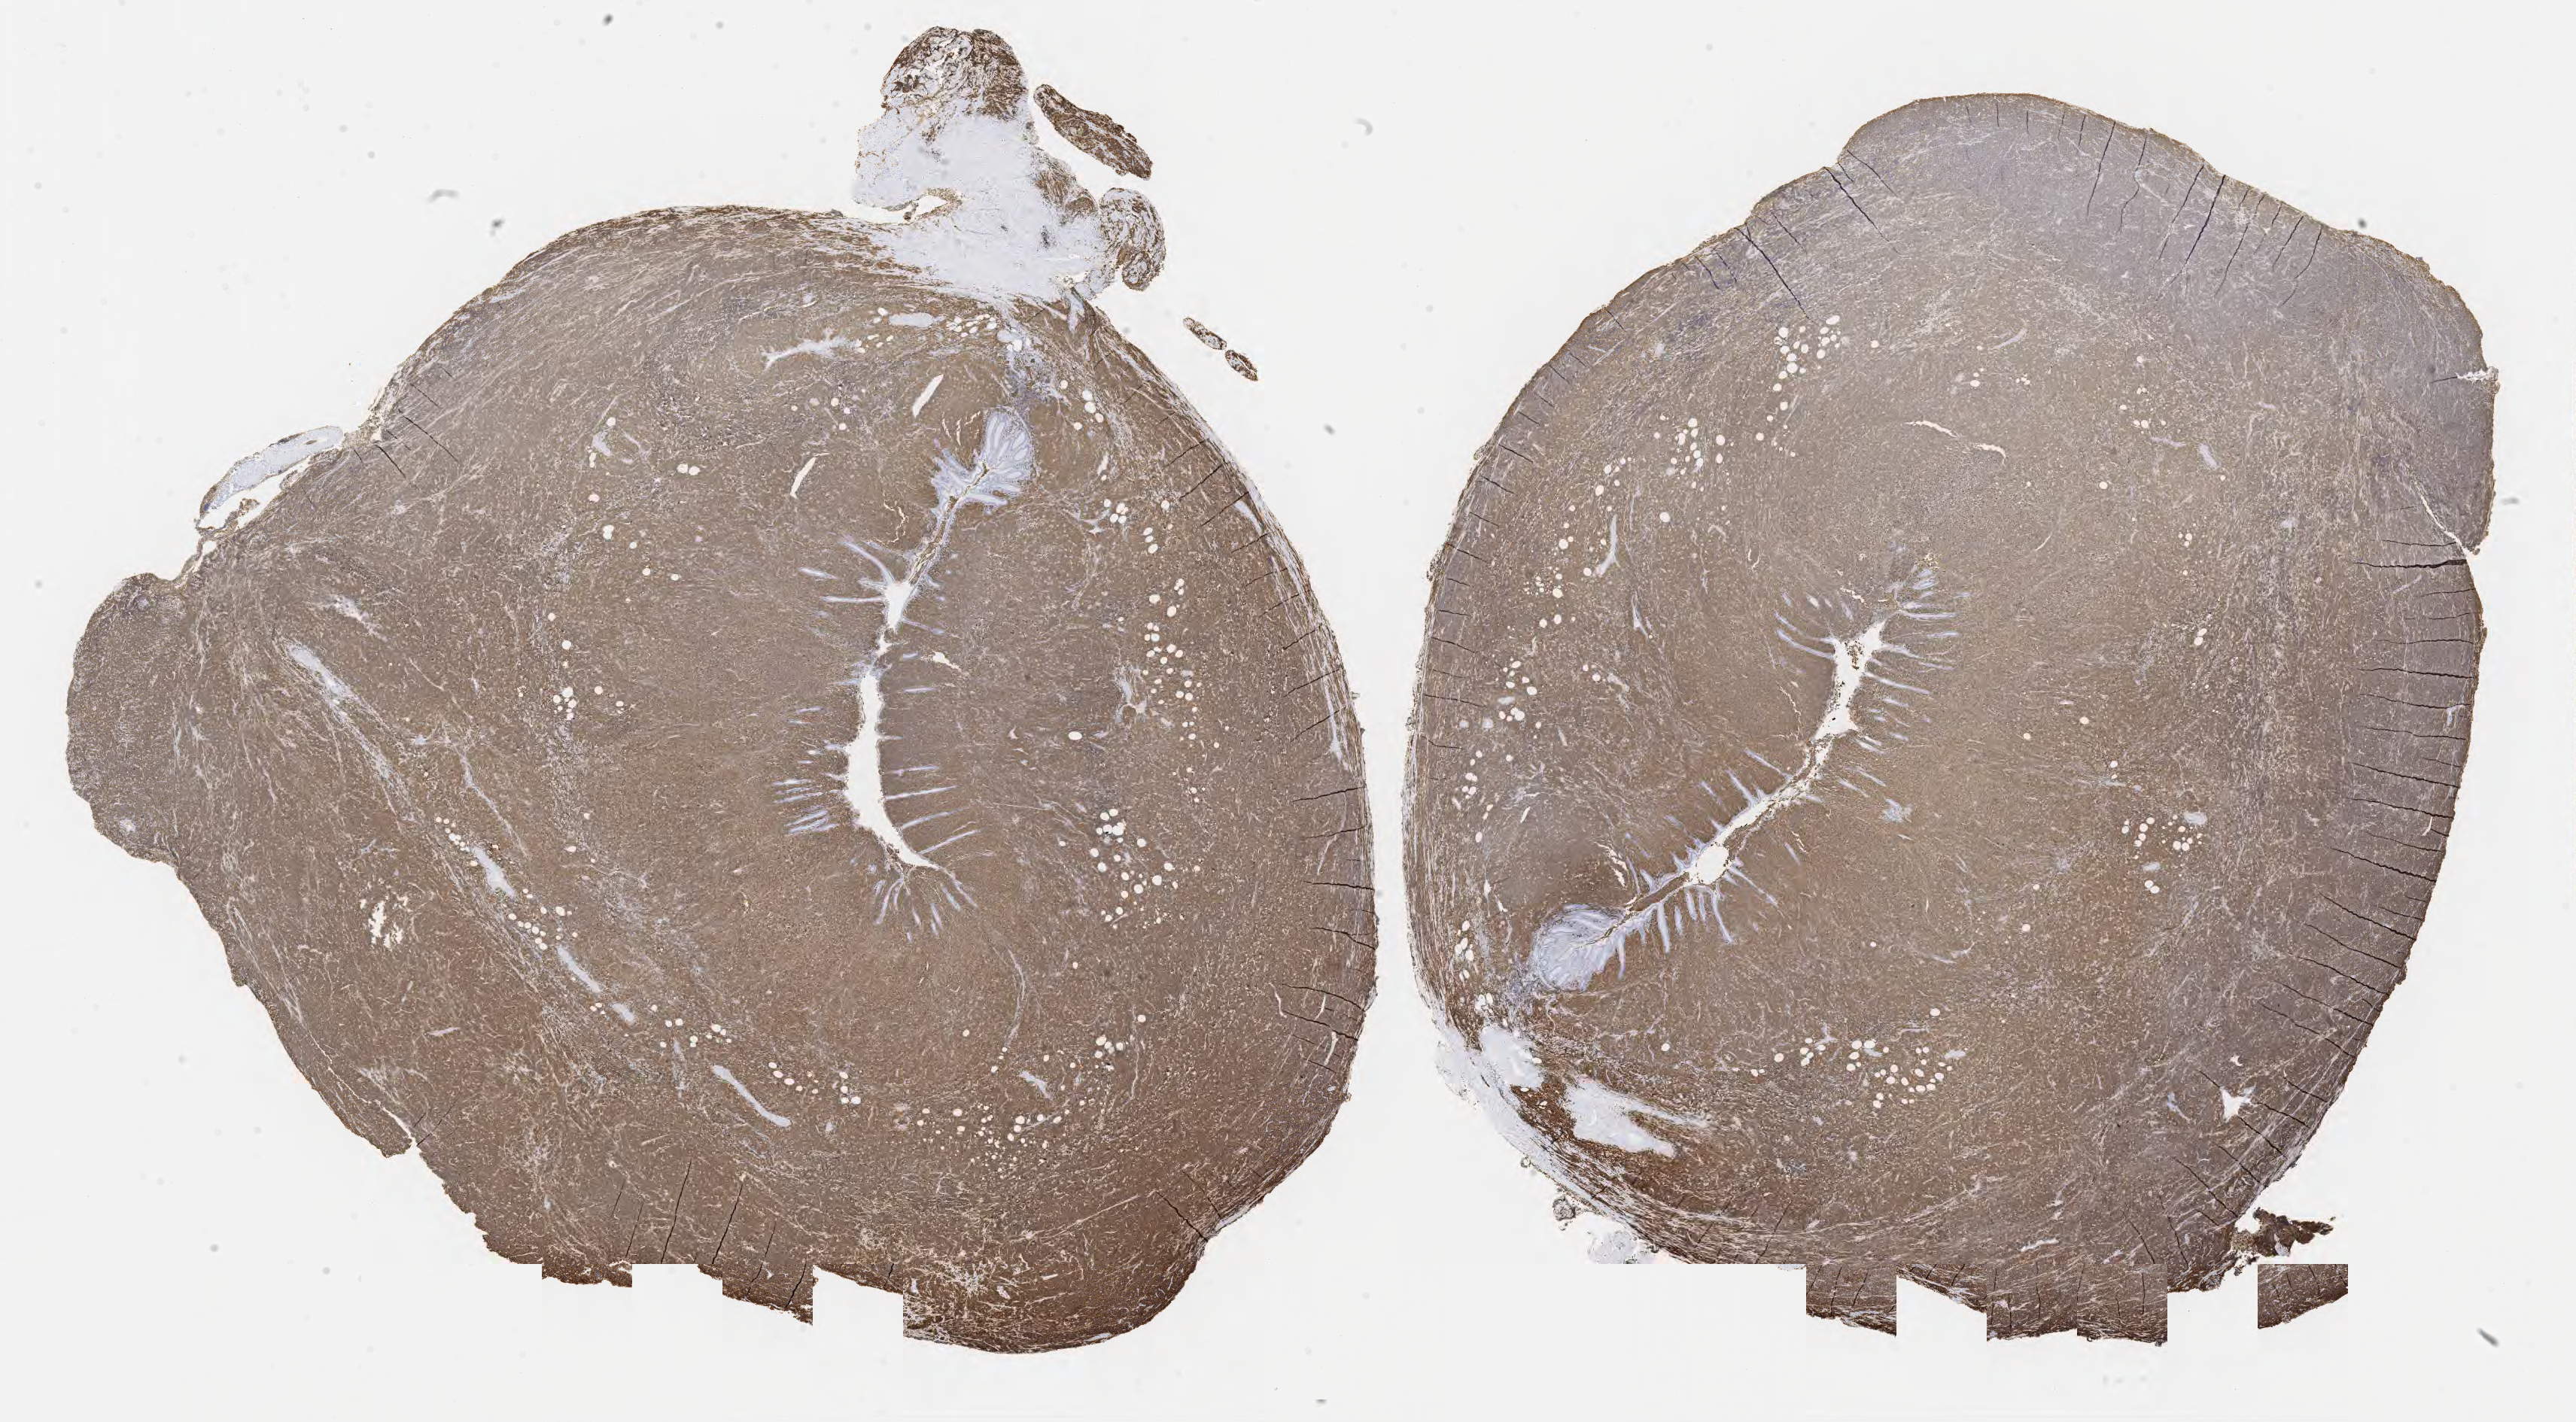
Immunohistochemistry (IHC) whole-slide image stained for CD20 — shown as a low-resolution overview of the whole scanned area (about 27.7 x 15.3 mm), tumor tissue. Patient: male, age 63 years.
* histologic diagnosis: Diffuse large B-cell lymphoma, NOS